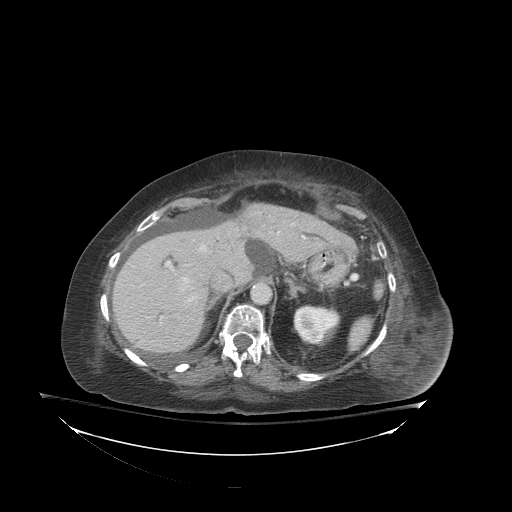
Contrast-enhanced abdominal CT (liver protocol), one axial slice. Slice 59 of 81 in the series (ordered by position). Reconstruction kernel STANDARD. Soft-tissue window (W 400 / L 40 HU). 2.5 mm slice thickness. 512 × 512 image matrix, field of view 500 × 500 mm. Case-level facts recorded for this patient, not image findings: diagnosis: hepatocellular carcinoma (patient treated with transarterial chemoembolisation; whether this scan precedes or follows treatment is not stated here); TNM stage (as recorded): Stage-I; Child-Pugh class: B.
Outlined on this slice (semi-automatically segmented with operator editing):
- liver parenchyma outside the tumour (the mass and vessels are separate outlines, so this box may not span the whole liver): bounding box <112,204,344,352> (left, top, right, bottom; pixels)
- liver vessels: <161,236,305,319>